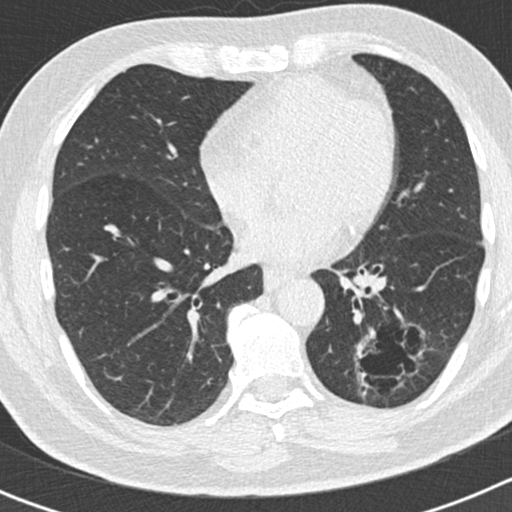
Axial slice from a low-dose chest CT screening exam; second screening round (one year after baseline); lung window (W 1500 / L -600 HU); 2 mm slice thickness; standard (soft-tissue) reconstruction kernel (B30f); slice 98 of 186 in the series. Male participant, aged 66 years at enrolment. Former smoker at enrolment.
Lesion marked by an expert reader, bounding box (x1, y1, x2, y2) in pixels: (347, 327, 416, 404). Screening reader's record for this exam (one nodule recorded; not confirmed to be the boxed lesion): non-calcified nodule or mass ≥4 mm, left lower lobe, 50 × 33 mm, smooth margins, pre-existing on the prior screen: yes; interval growth: yes. Official screen result: positive, other.